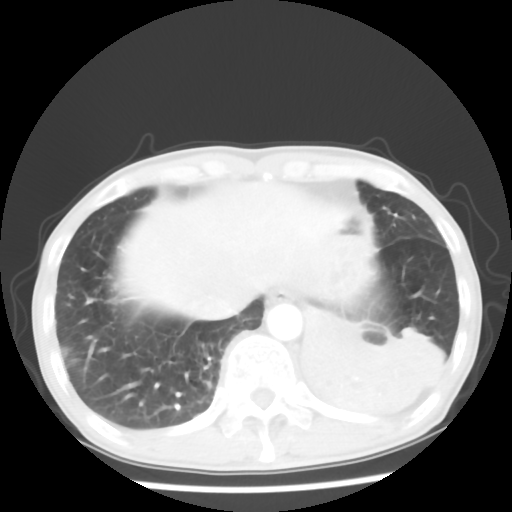
Chest CT, one axial slice; reconstruction kernel STANDARD; lung window (W 1500 / L -600 HU); 5 mm slice thickness; 512 × 512 image matrix, field of view 313 × 313 mm. Male patient, age 68 years. From the clinical record (not read from this slice): clinical TNM (as recorded): T4 N0 M0.
Outlined on this slice (rectangle marked by the reading radiologist):
- lung tumour (recorded histology: squamous cell carcinoma): bounding box <289,298,452,441> (left, top, right, bottom; pixels)